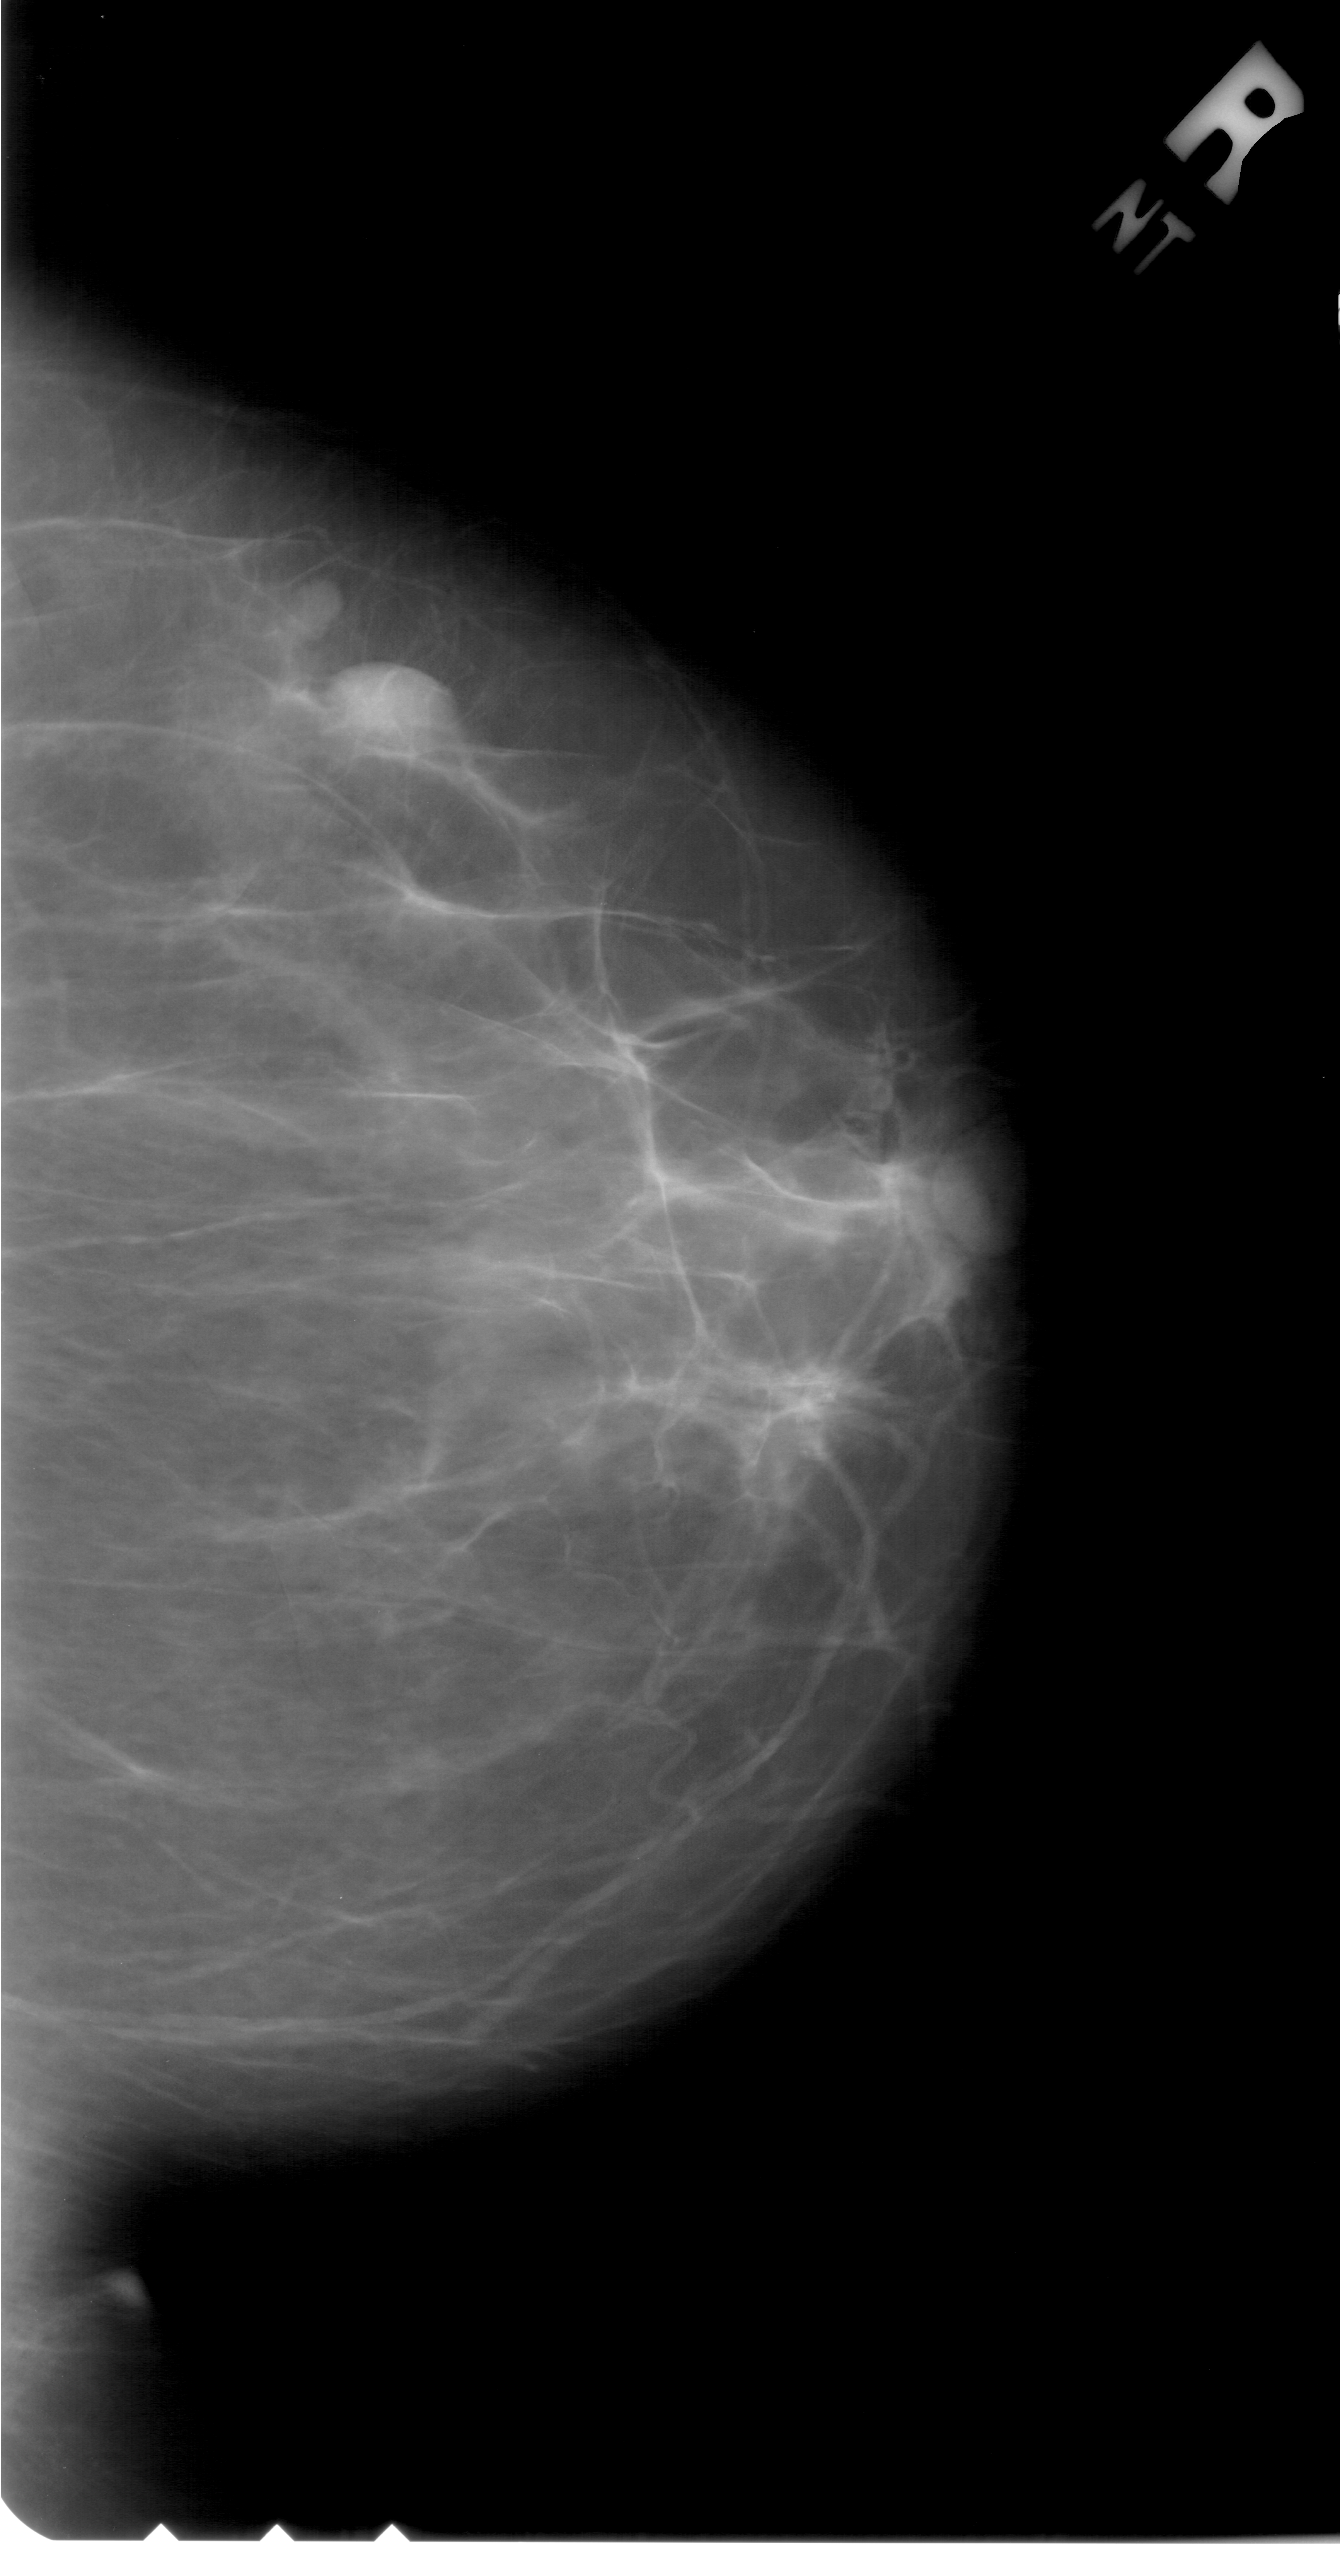
Digitized screen-film mammogram, right breast, CC view.
- Mass, shape oval, margins obscured; BI-RADS assessment category 4; subtlety rating 4 on a 1 (subtle) to 5 (obvious) scale; pathology result (as recorded, not read from the image): benign.